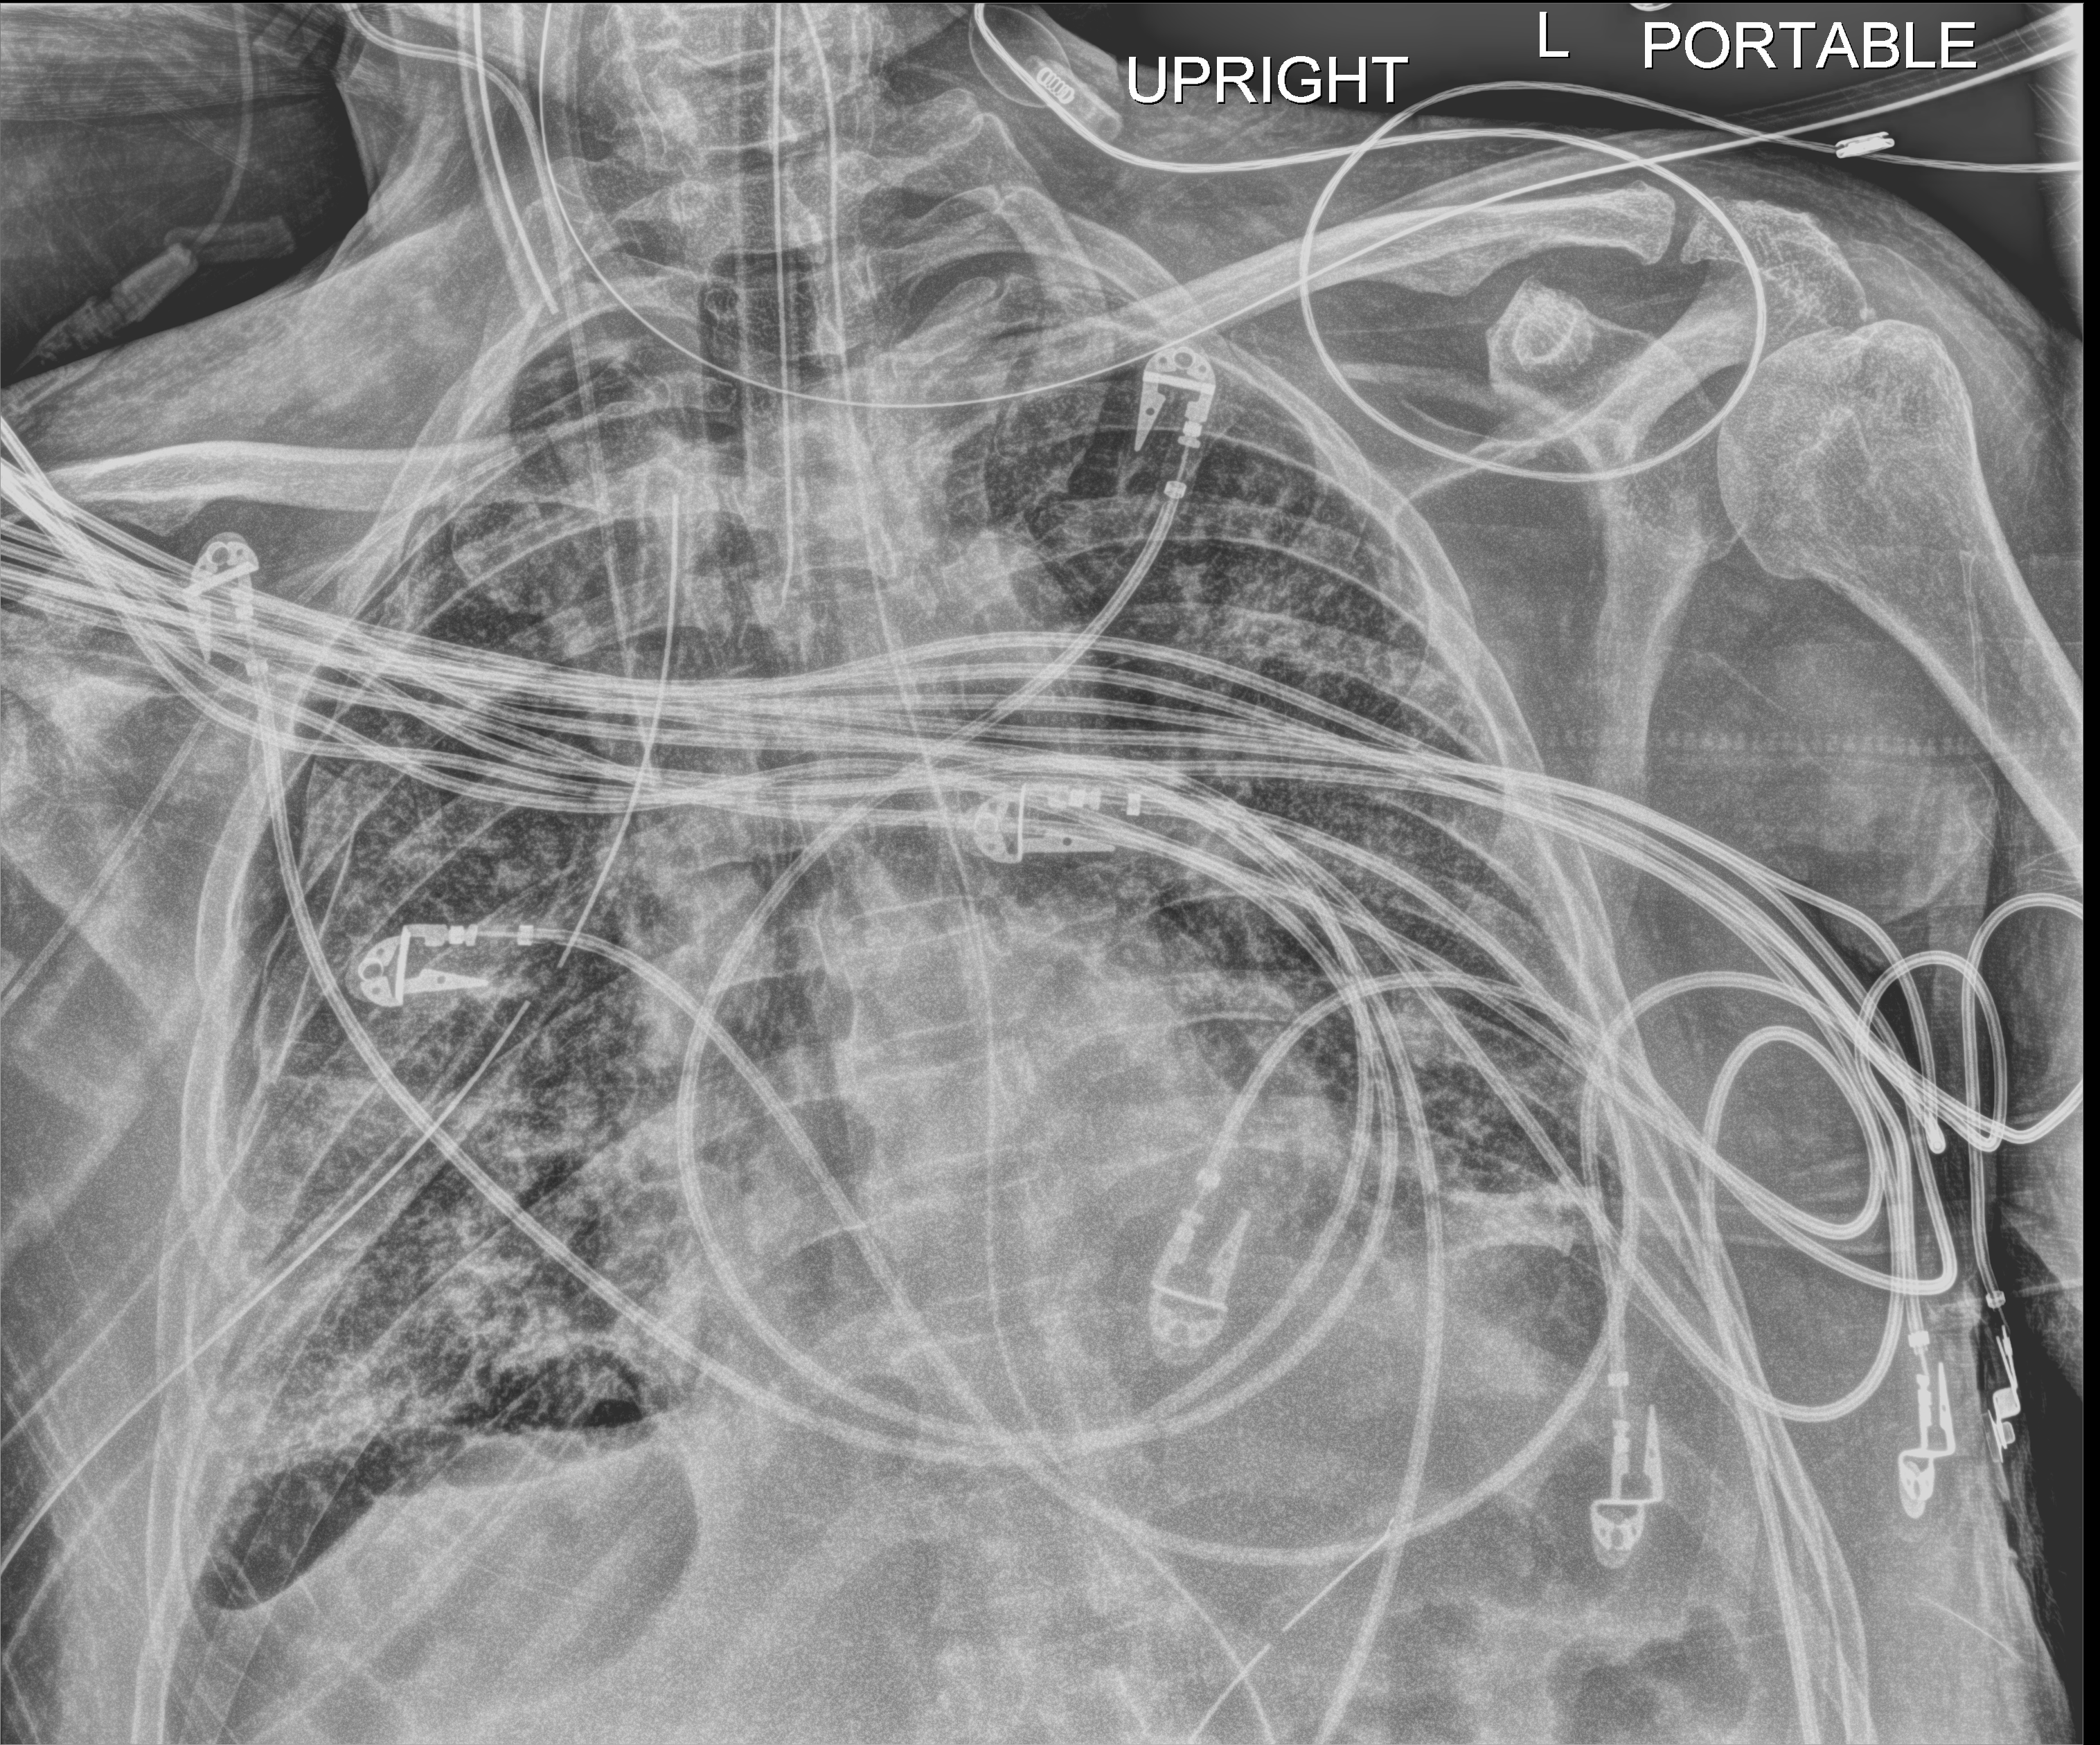
Portable chest radiograph. Male patient hospitalised with COVID-19, age 60–74 years.
Admission-level facts for this patient (not findings on this image; timing relative to this image not recorded): length of hospital stay: 37 days.